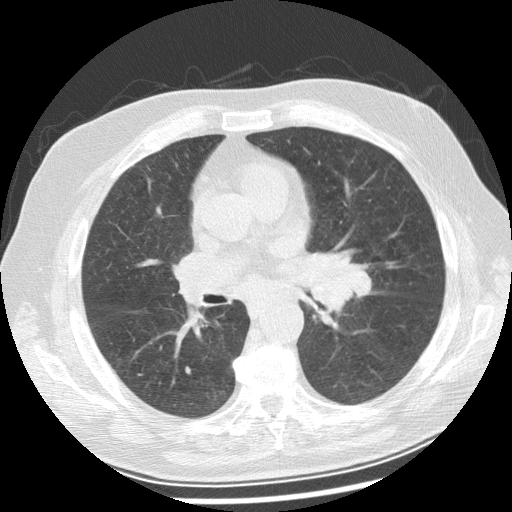
Low-dose screening chest CT, one axial slice; position 138 of 250 along the scan axis; reconstruction kernel STANDARD; 120 kVp; lung window (W 1500 / L -600 HU); 512 × 512 image matrix, field of view 360 × 360 mm.
Structures marked on this image (outlined manually by an expert reader):
- lesion 1 (tumor, left main bronchus): bounding box (x1, y1, x2, y2) in pixels: (312, 266, 371, 313)